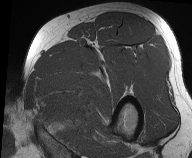
MRI of an extremity soft-tissue mass, one axial slice; position 45 of 61 along the scan axis; MR volume resampled by the dataset authors to the PET/CT grid (not the native acquisition matrix); 192 × 158 image matrix, field of view 187 × 154 mm. Male patient. From the clinical record (not read from this slice): histological type: pleiomorphic liposarcoma; grade: high; site of the primary tumour: left thigh.
Outlined on this slice (expert contour drawn on MRI and transferred to this co-registered scan by the dataset authors):
- gross tumour volume including surrounding oedema: bounding box <32,83,67,125> (left, top, right, bottom; pixels)